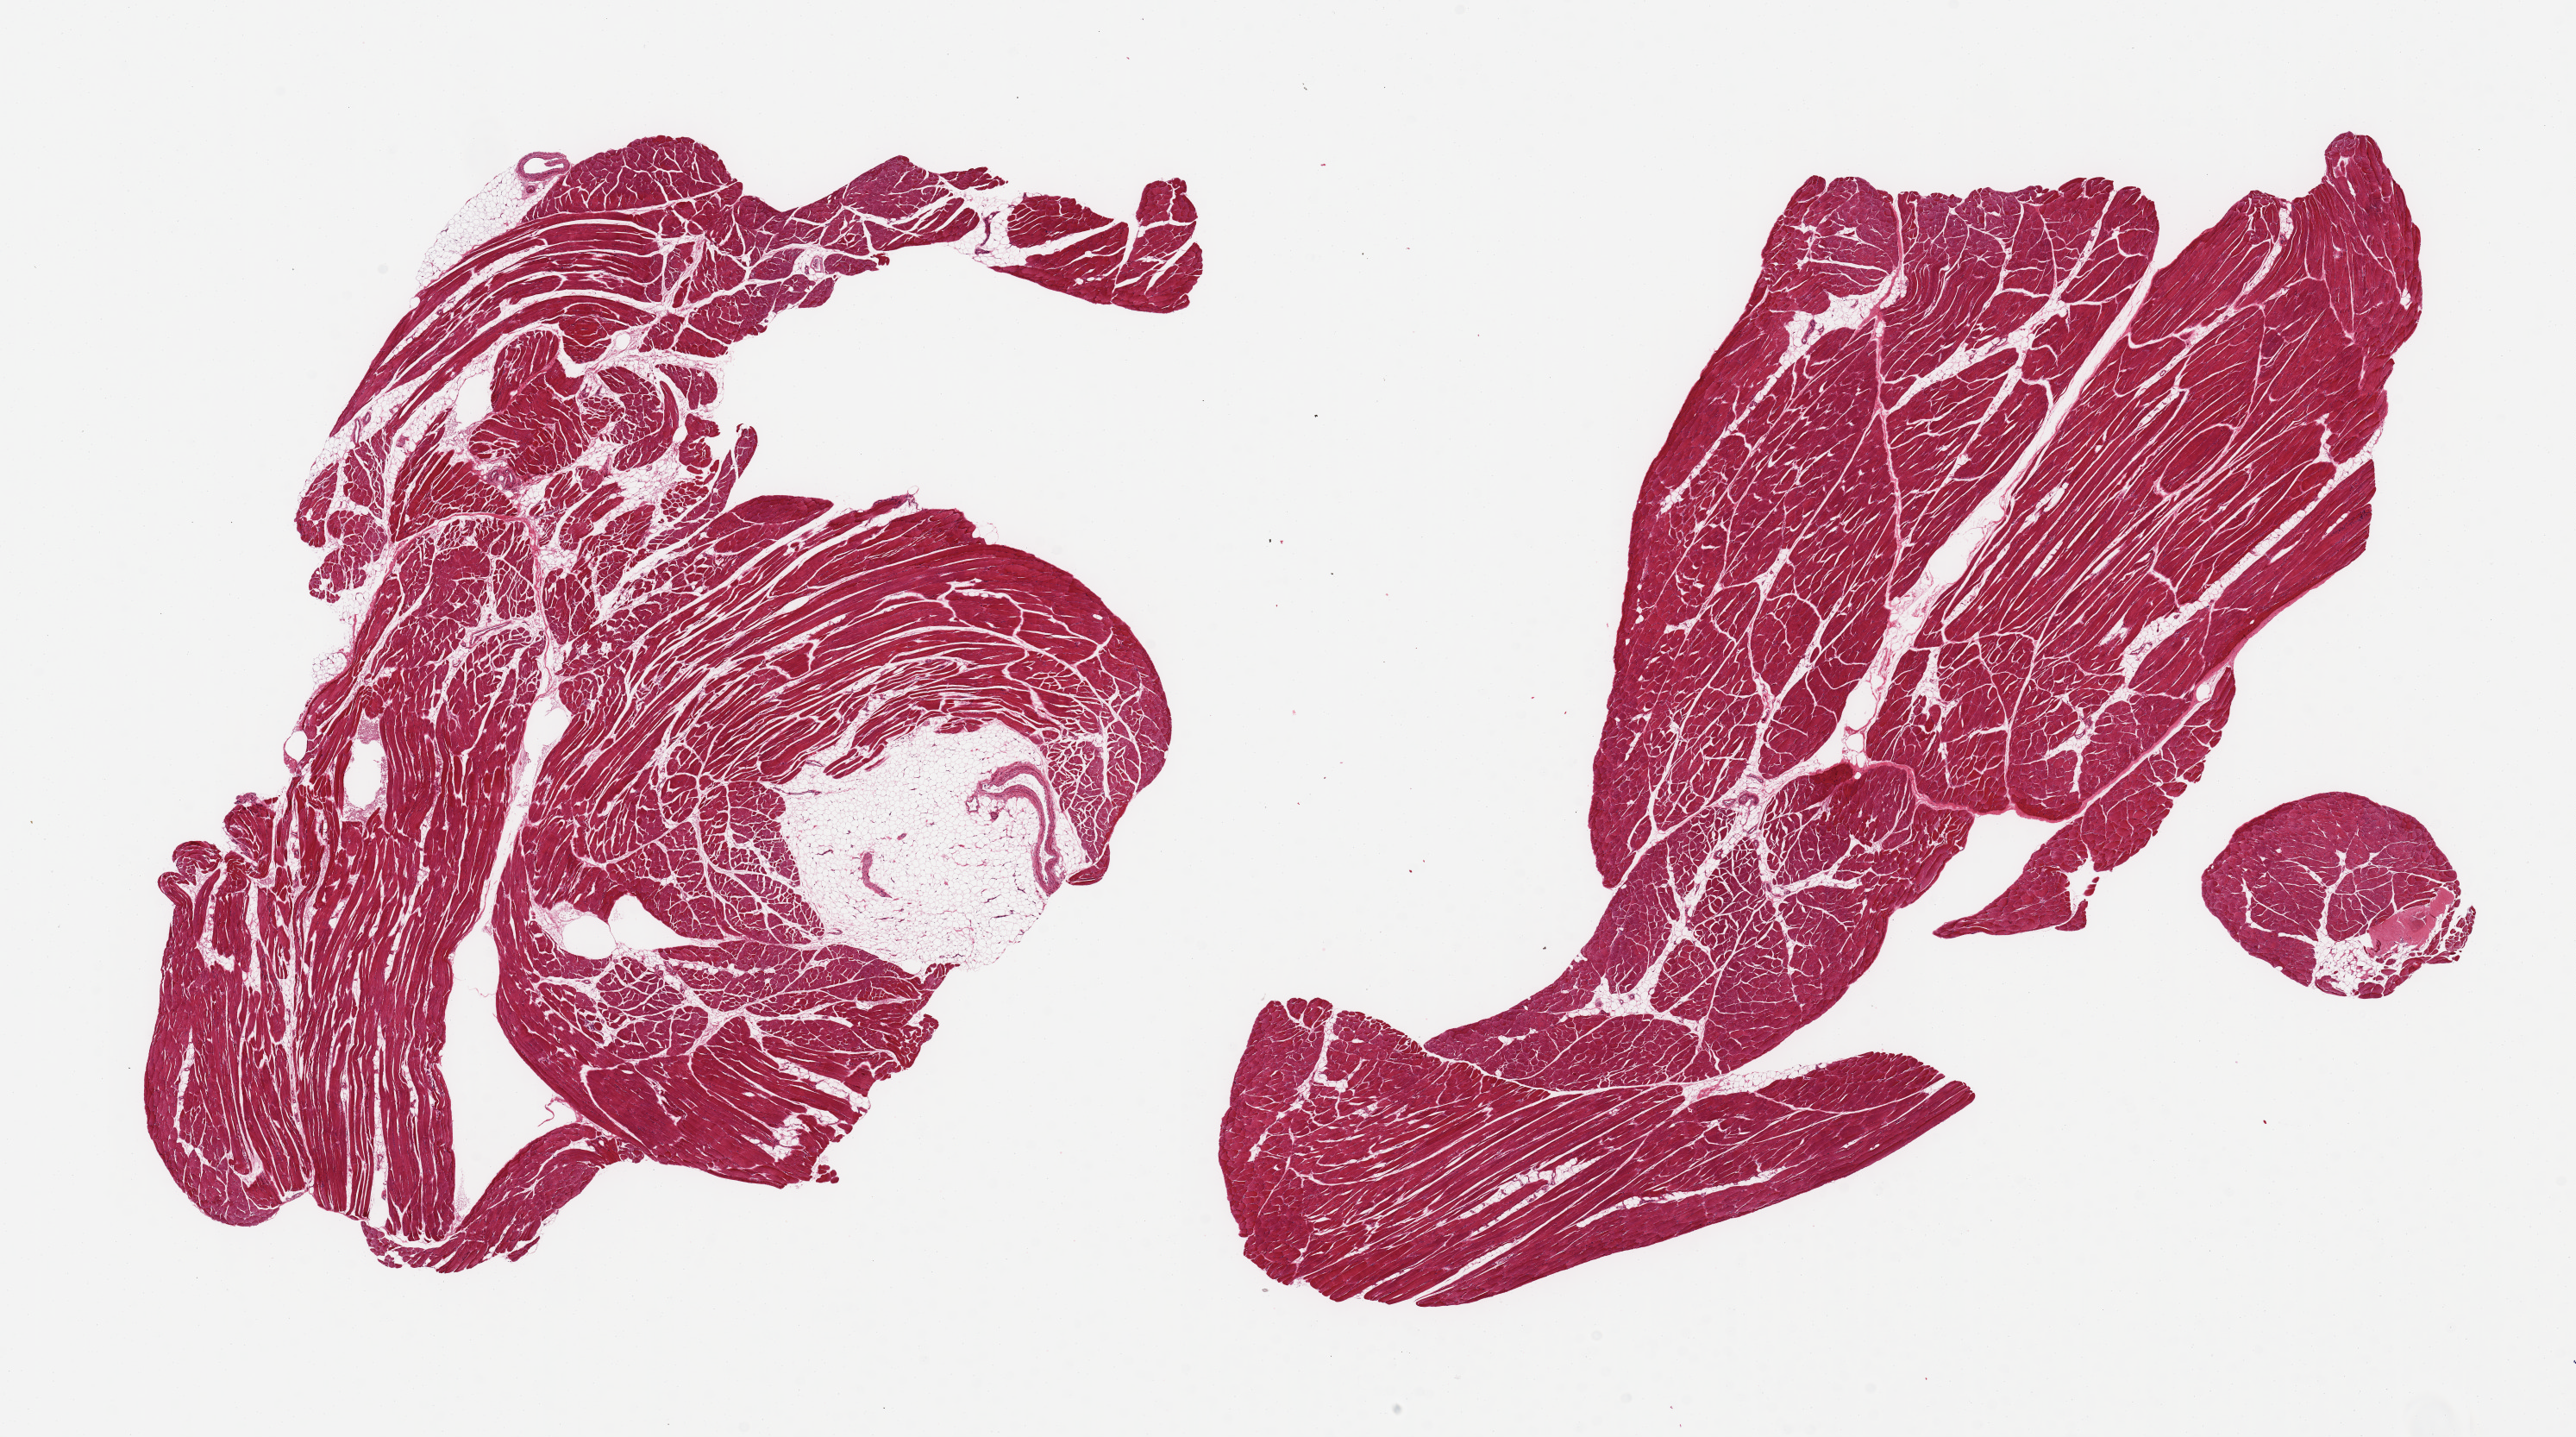
Digitized haematoxylin and eosin-stained section, shown as a low-resolution overview of the whole scanned area (about 23.6 x 13.2 mm). PAXgene-fixed paraffin-embedded (PFPE) section. Target tissue: skeletal muscle. Donor tissue sample. Donor sex: male.
Review note (as recorded): 2 pieces, ~15-20% interstitial fat.